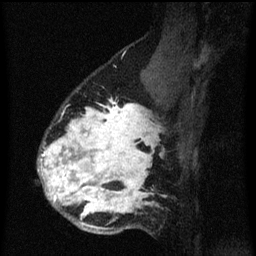
Breast MRI (dynamic contrast-enhanced), one sagittal slice; slice 45 of 60 in the series (ordered by position); dynamic contrast-enhanced series, image 2 of 3 at this slice position (ordered by acquisition); 1.5 T; TE 4.2 ms, TR 8.4 ms; 2 mm slice thickness; 256 × 256 image matrix, field of view 180 × 180 mm. Patient: female, 34 years. Case-level facts recorded for this patient, not image findings: setting: breast cancer imaged before/during neoadjuvant chemotherapy; receptor status: HR-positive, HER2-negative.
Annotated regions visible in this slice (semi-automatic segmentation, software-assisted and operator-edited):
- analysis volume of interest (the breast-tissue region the enhancement analysis was run in; not a lesion): bounding box [x1, y1, x2, y2] px = [38, 58, 173, 235]
- tumour enhancement mask (voxels above the 70 % enhancement threshold inside the analysis volume of interest): [40, 100, 157, 229]